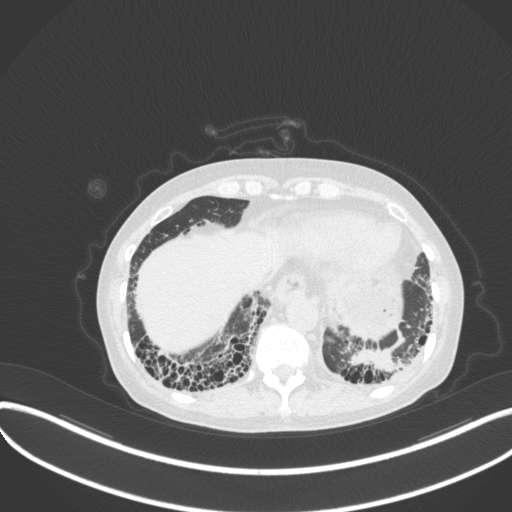
Chest CT, one axial slice; slice 60 of 373 in the series (ordered by position); reconstruction kernel B31f; lung window (W 1500 / L -600 HU); 512 × 512 image matrix, field of view 400 × 400 mm. Patient: female, 56 years. From the clinical record (not read from this slice): clinical TNM (as recorded): T1 N0 M0.
Annotated regions visible in this slice (bounding box drawn by a radiologist):
- lung tumour (recorded histology: adenocarcinoma): bounding box <339,344,417,375> (left, top, right, bottom; pixels)